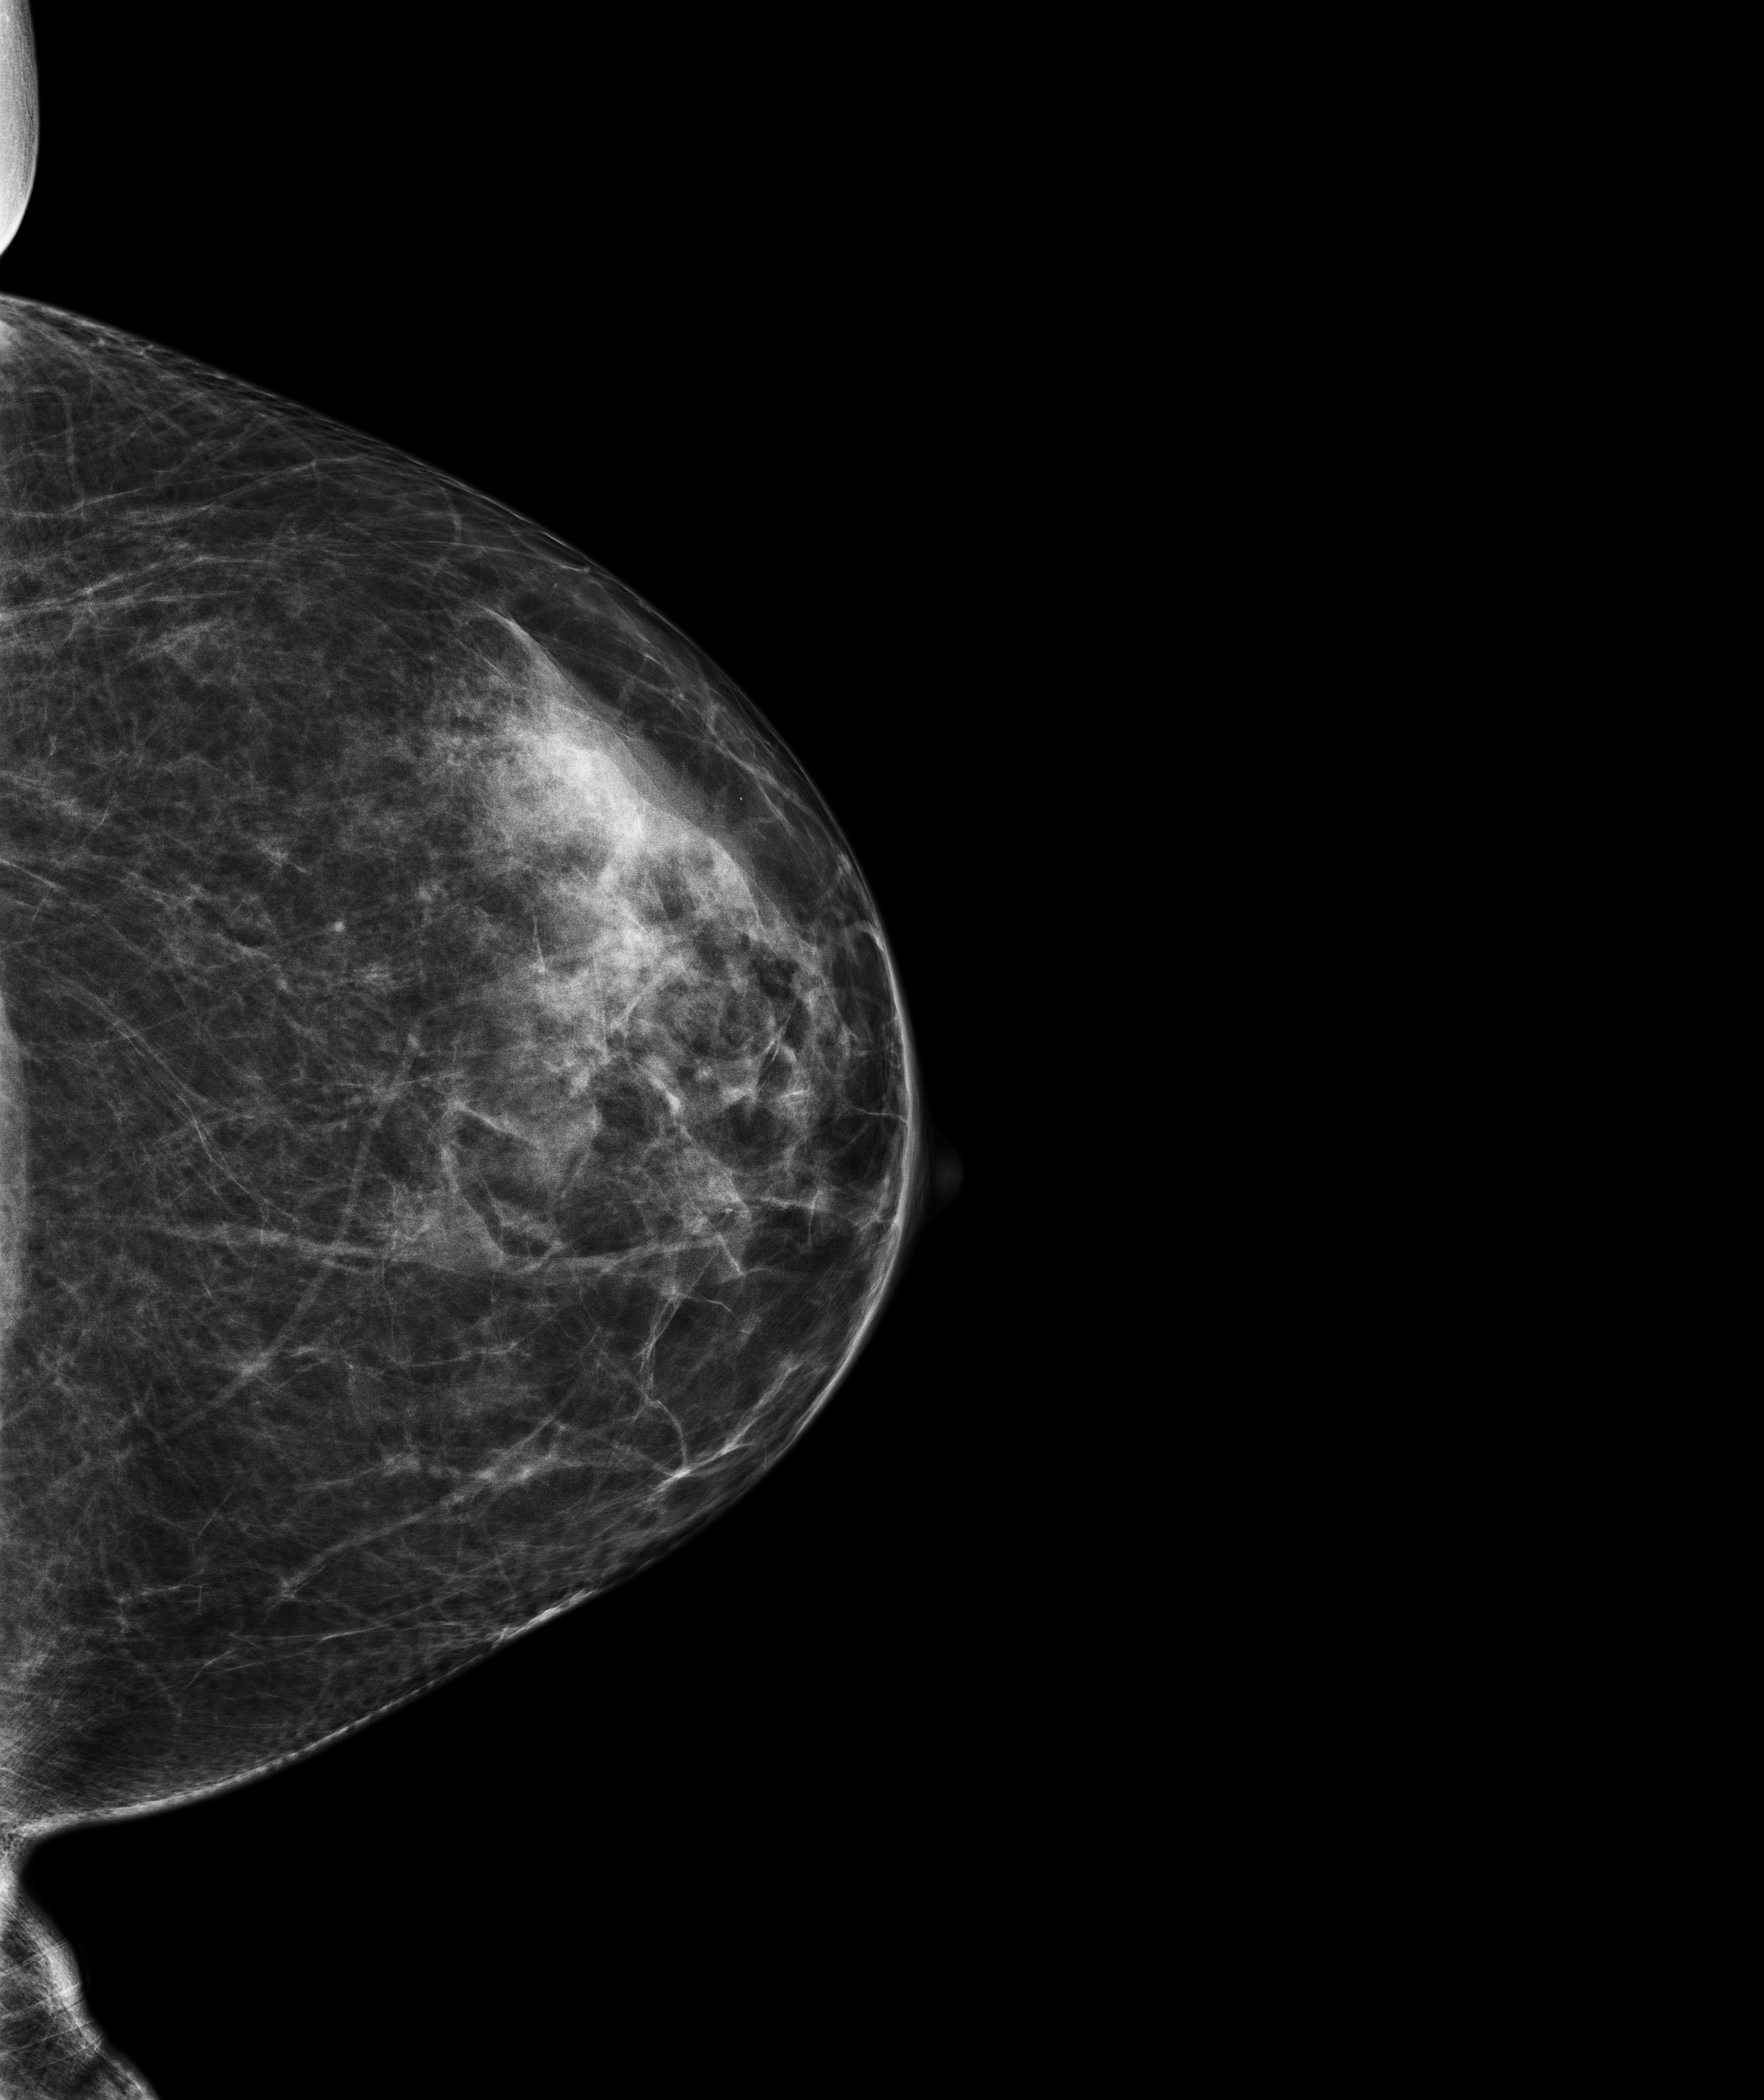
Annual screening mammography examination; system: Senographe Pristina. Patient: female, 49 years.
Image type: full-field digital mammogram. Breast: left. Projection: CC view.